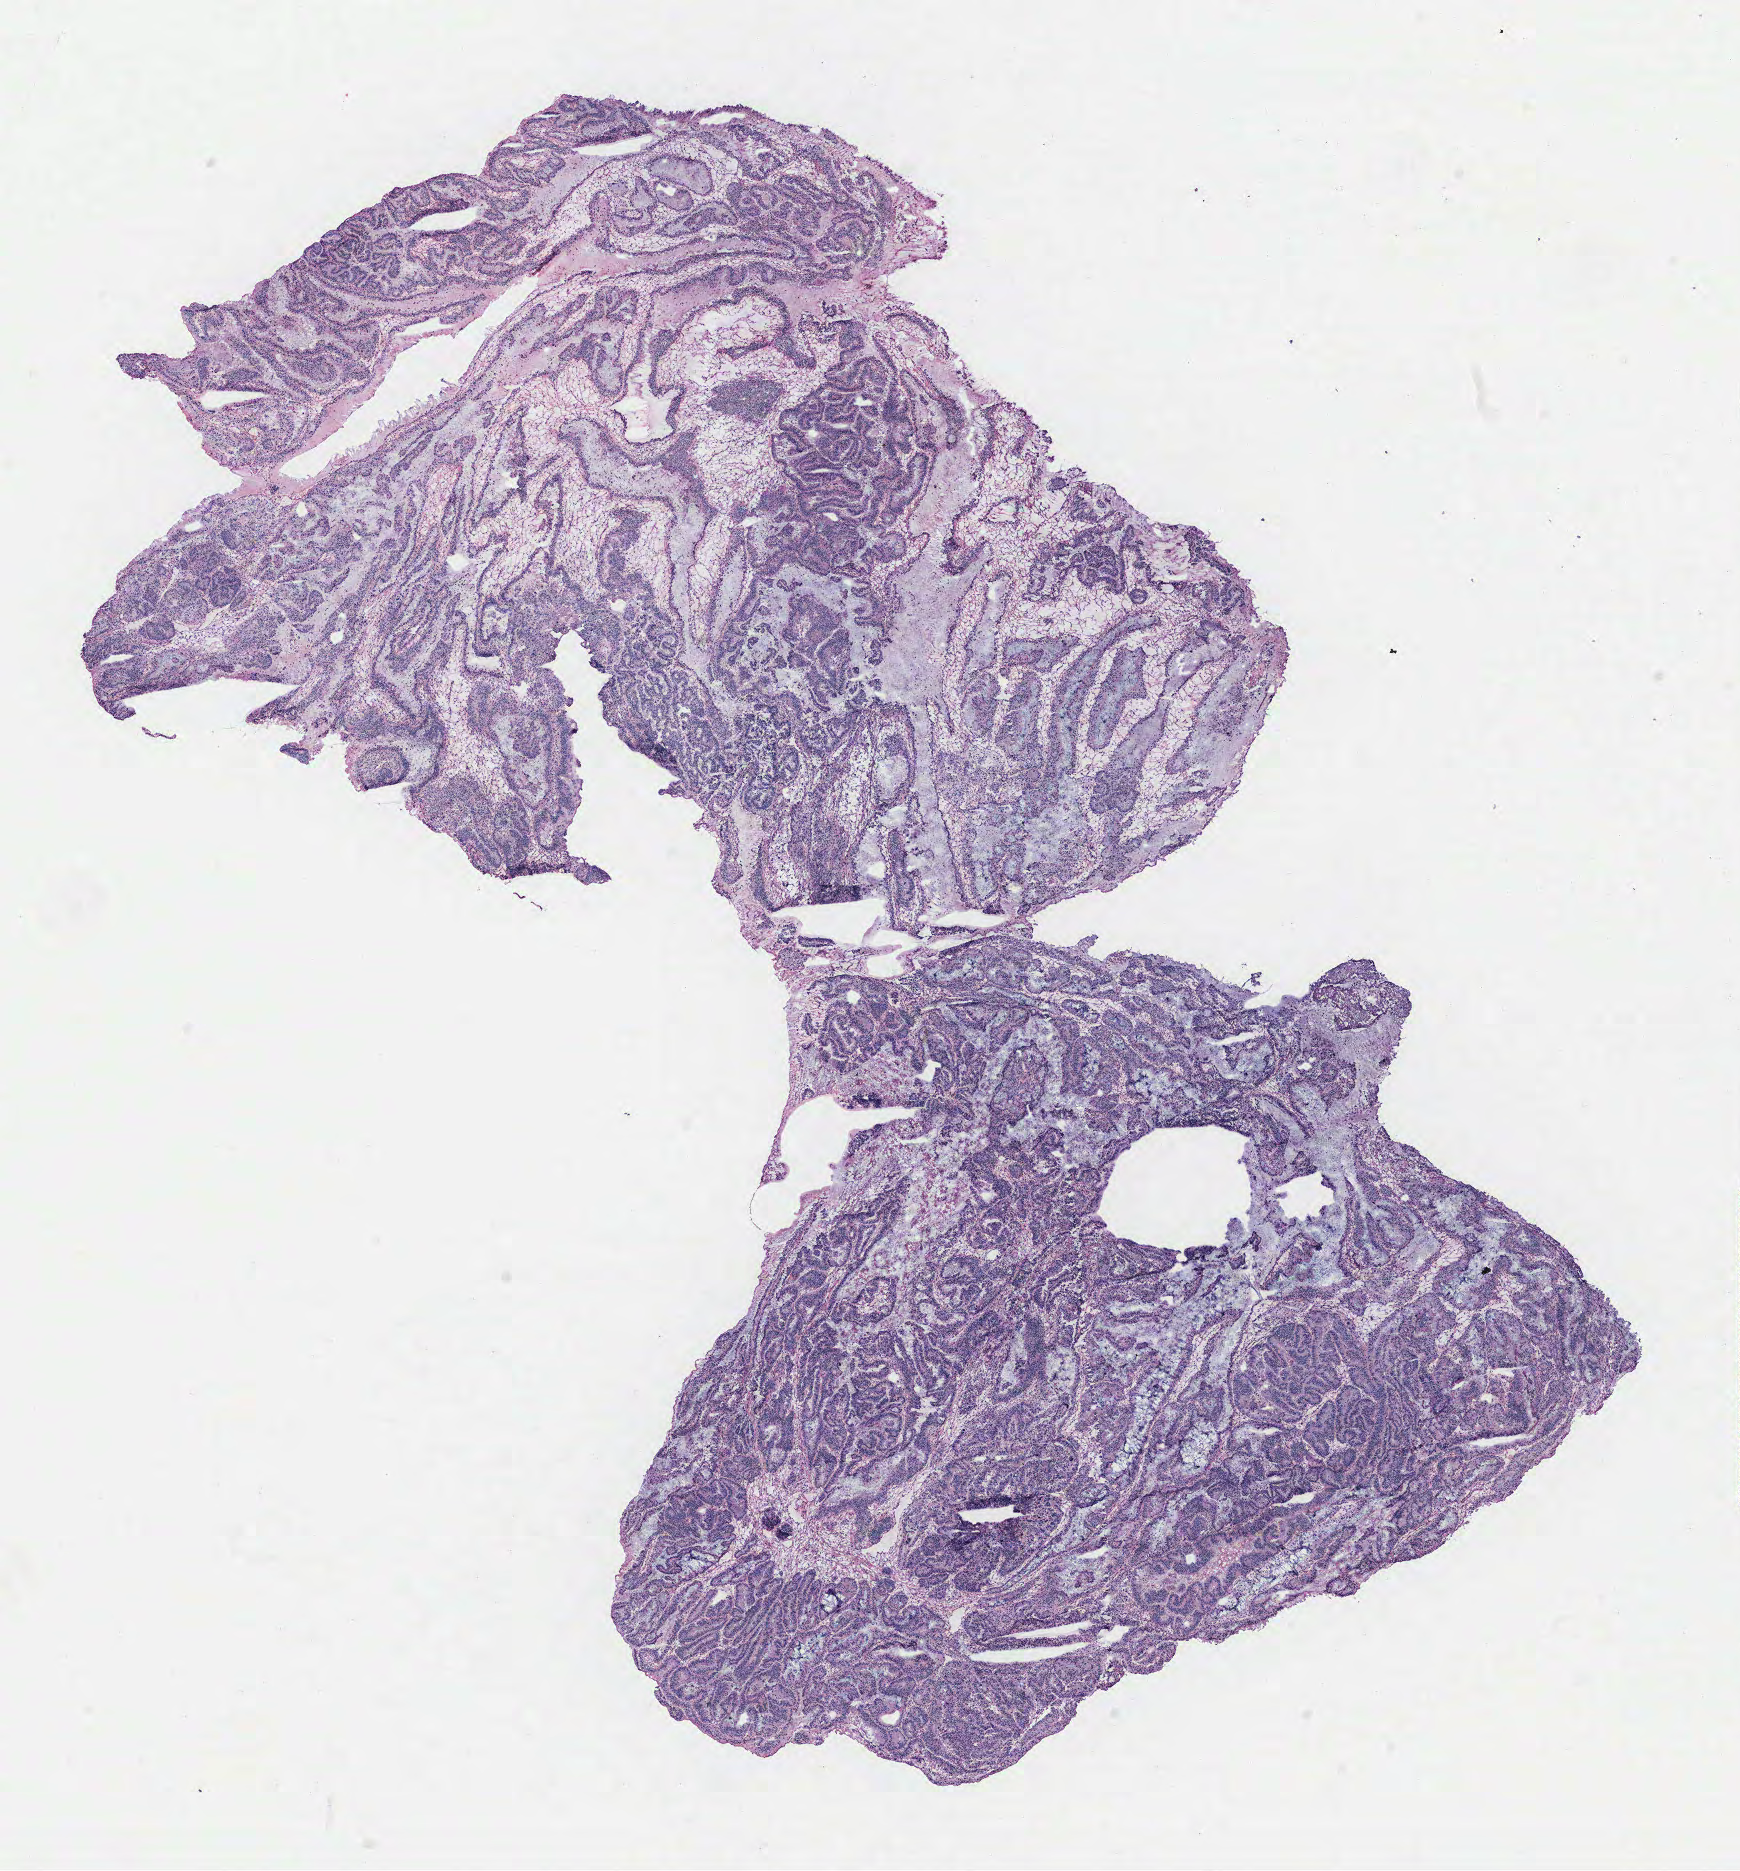
Hematoxylin and eosin (H&E) stained whole-slide image, whole scanned area (about 13.9 x 15.0 mm) shown as a low-resolution overview; ovary, normal (non-tumour) tissue. Female, 48 y/o.
- this section: normal (non-tumour) tissue from the same patient
- patient diagnosis: Serous adenocarcinoma, NOS